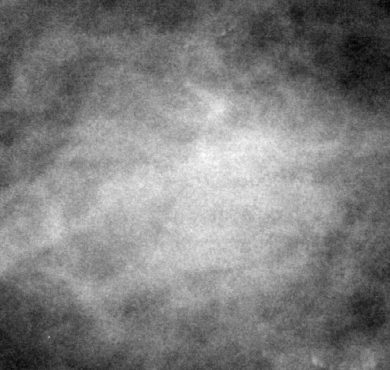
Crop from a digitized film mammogram around one marked abnormality; right breast; MLO view.
Marked abnormality: mass, shape round, margins ill defined; BI-RADS assessment category 5; subtlety rating 5 on a 1 (subtle) to 5 (obvious) scale; pathology result (as recorded, not read from the image): malignant.